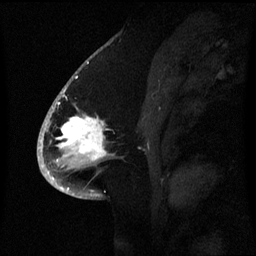
Breast MRI (dynamic contrast-enhanced), one sagittal slice. Dynamic contrast-enhanced series, image 2 of 3 at this slice position (ordered by acquisition). 1.5 T. TE 4.2 ms, TR 8.4 ms. 2.1 mm slice thickness. 256 × 256 image matrix. Patient: female, 53 years. Case-level facts recorded for this patient, not image findings: setting: breast cancer imaged before/during neoadjuvant chemotherapy; receptor status: HR-positive, HER2-negative.
Annotated regions visible in this slice (semi-automatically segmented with operator editing):
- analysis volume of interest (the breast-tissue region the enhancement analysis was run in; not a lesion): bounding box (x1, y1, x2, y2) in pixels: (52, 90, 122, 171)
- tumour enhancement mask (voxels above the 70 % enhancement threshold inside the analysis volume of interest): (58, 90, 107, 161)